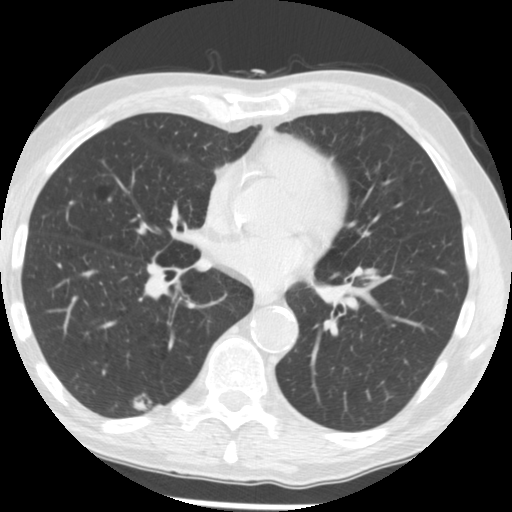
Axial slice from a low-dose chest CT screening exam; second screening round (one year after baseline); lung window (W 1500 / L -600 HU); 2.5 mm slice thickness; standard (soft-tissue) reconstruction kernel (STANDARD); slice 91 of 173 in the series. Male participant, aged 62 years at enrolment.
Expert-annotated lung lesion, bounding box (x1, y1, x2, y2) in pixels: (124, 388, 161, 423). The screening reader recorded 2 non-calcified nodules or masses ≥4 mm on this exam (right lower lobe, right lower lobe); which of them this box marks is not recorded. Participant outcome: lung cancer diagnosed 506 days after this screen — adenocarcinoma, NOS, right lower lobe, moderately differentiated (G2), stage IIIB (AJCC 6th edition), 15 mm at pathology.